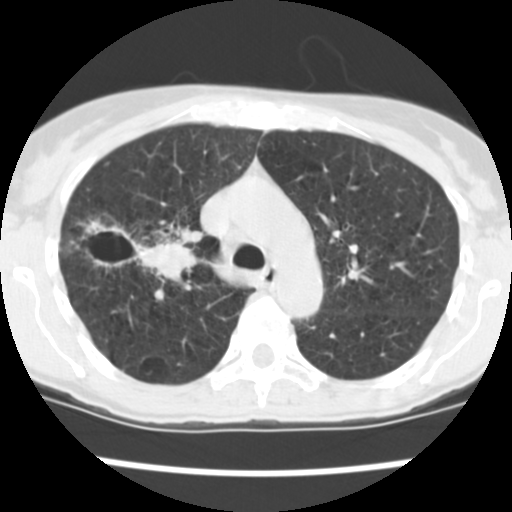
Low-dose screening chest CT, one axial slice; position 172 of 252 along the scan axis; lung window (W 1500 / L -600 HU); 2.5 mm slice thickness; 512 × 512 image matrix, field of view 276 × 276 mm.
Annotated regions visible in this slice (manually delineated by an expert):
- lesion 2 (tumor, lower lobe of right lung): bounding box [x1, y1, x2, y2] px = [85, 220, 202, 283]